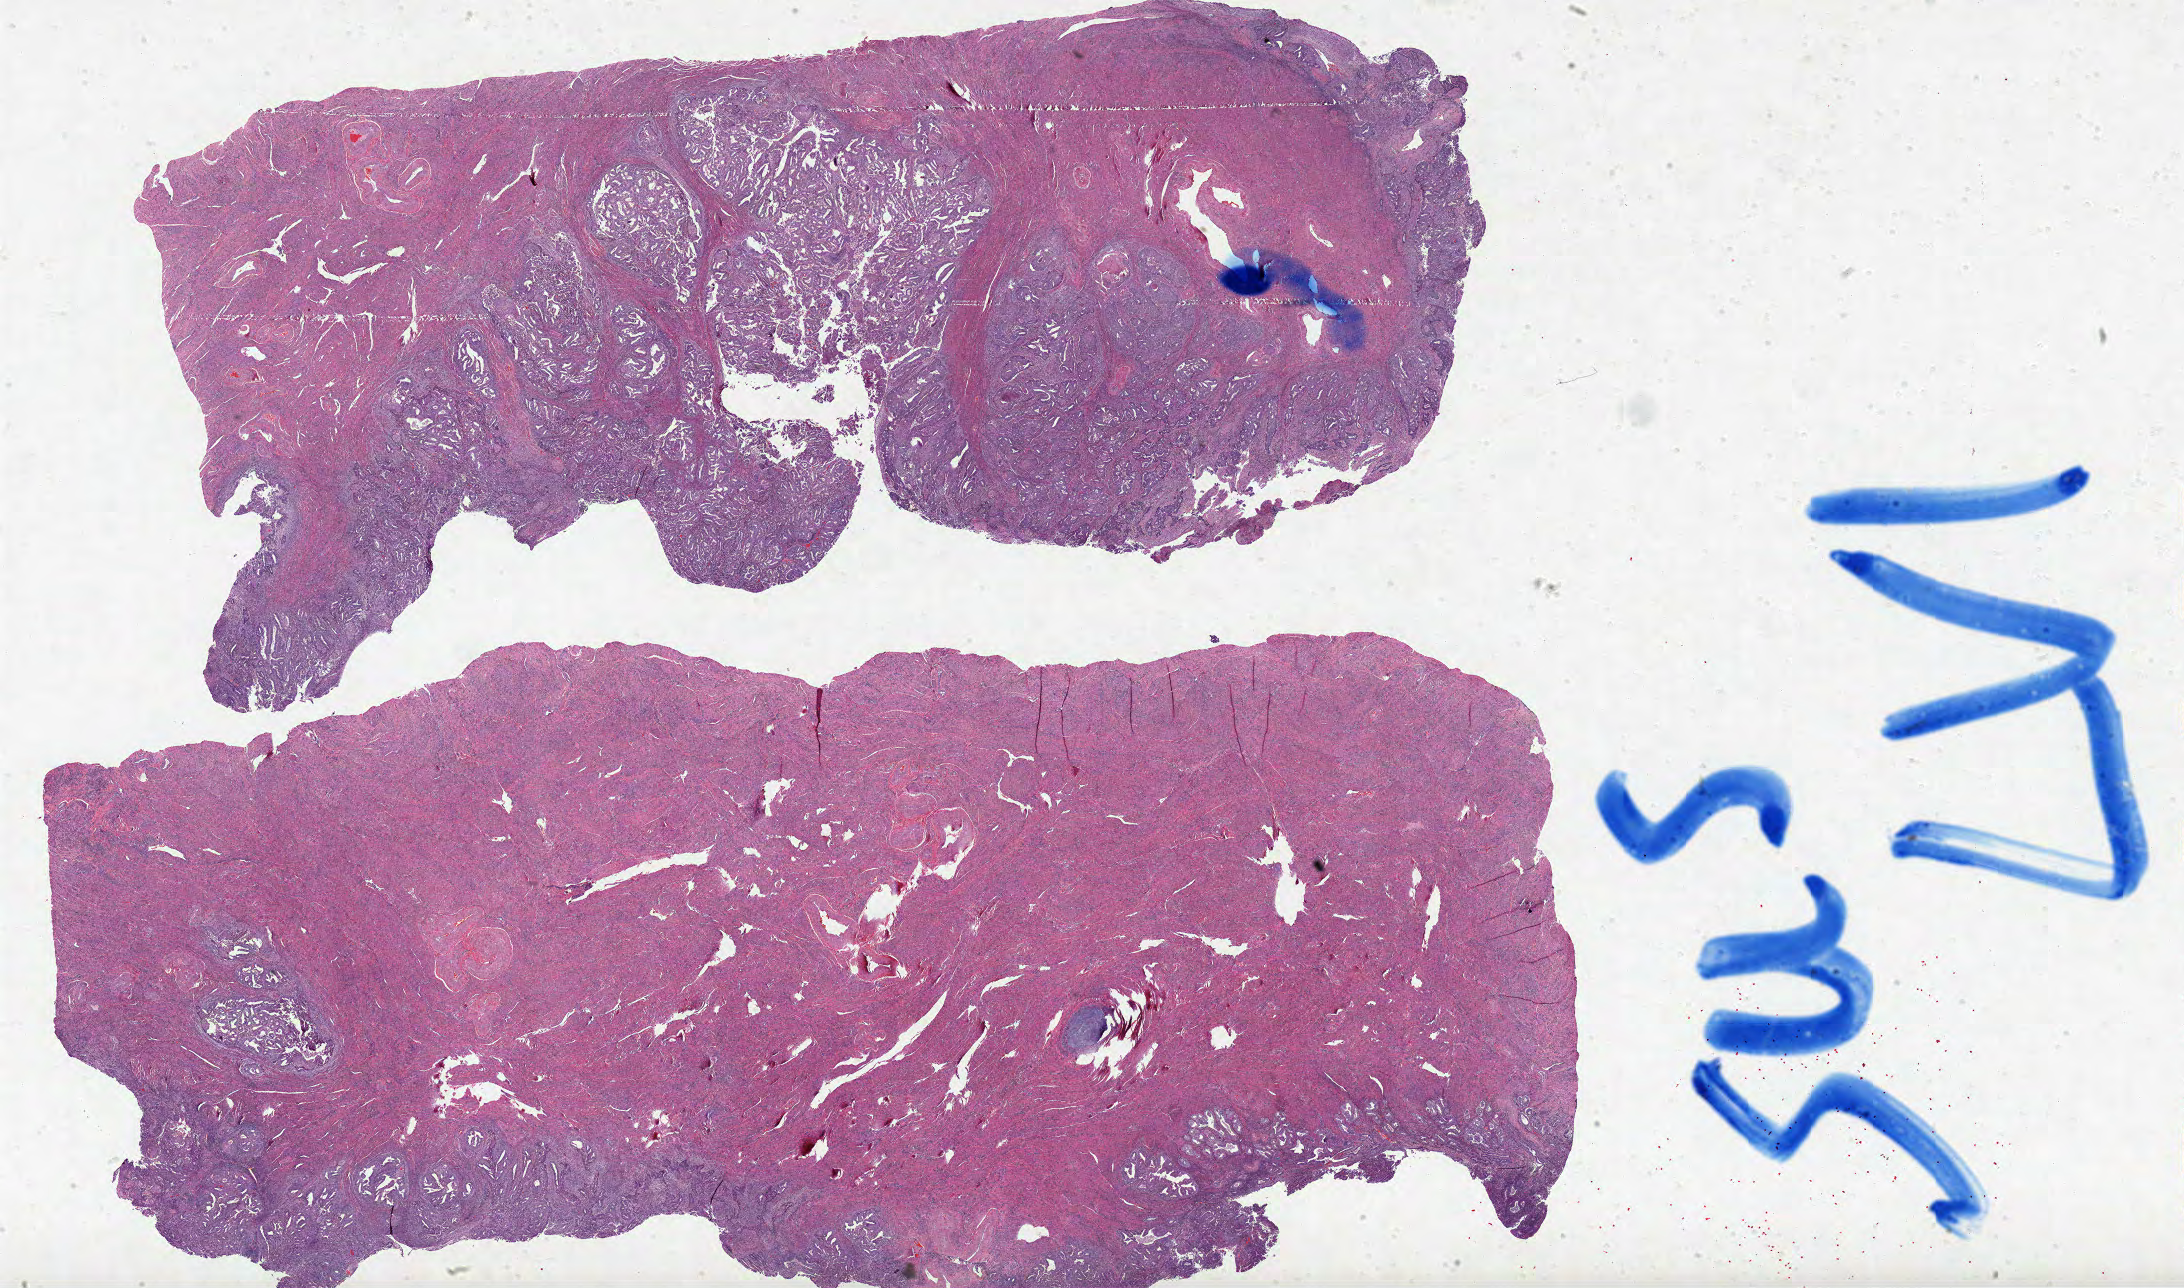
Digitized Hematoxylin and eosin (H&E) stained tissue section (whole slide), low-resolution overview of the scanned area, about 34.8 x 20.5 mm; formalin-fixed paraffin-embedded (FFPE) diagnostic section; primary tumour sample from the uterus. Female patient; age at initial diagnosis 58 years. Histologic grade: G1 (well differentiated).
FIGO stage: IA. Pathologic diagnosis: Endometrioid adenocarcinoma, NOS (endometrium).